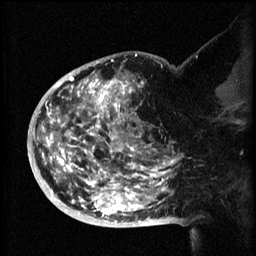
Breast MRI (dynamic contrast-enhanced), one sagittal slice; position 38 of 60 along the scan axis; 3 images stored at this slice position (order not interpretable as contrast timing); 1.5 T; TE 4.2 ms, TR 8.2 ms; 2 mm slice thickness; 256 × 256 image matrix. Patient: female, 50 years.
Outlined on this slice (semi-automatically segmented with operator editing):
- analysis volume of interest (the breast-tissue region the enhancement analysis was run in; not a lesion): bounding box <44,72,173,219> (left, top, right, bottom; pixels)
- tumour enhancement mask (voxels above the 70 % enhancement threshold inside the analysis volume of interest): <44,72,173,219>